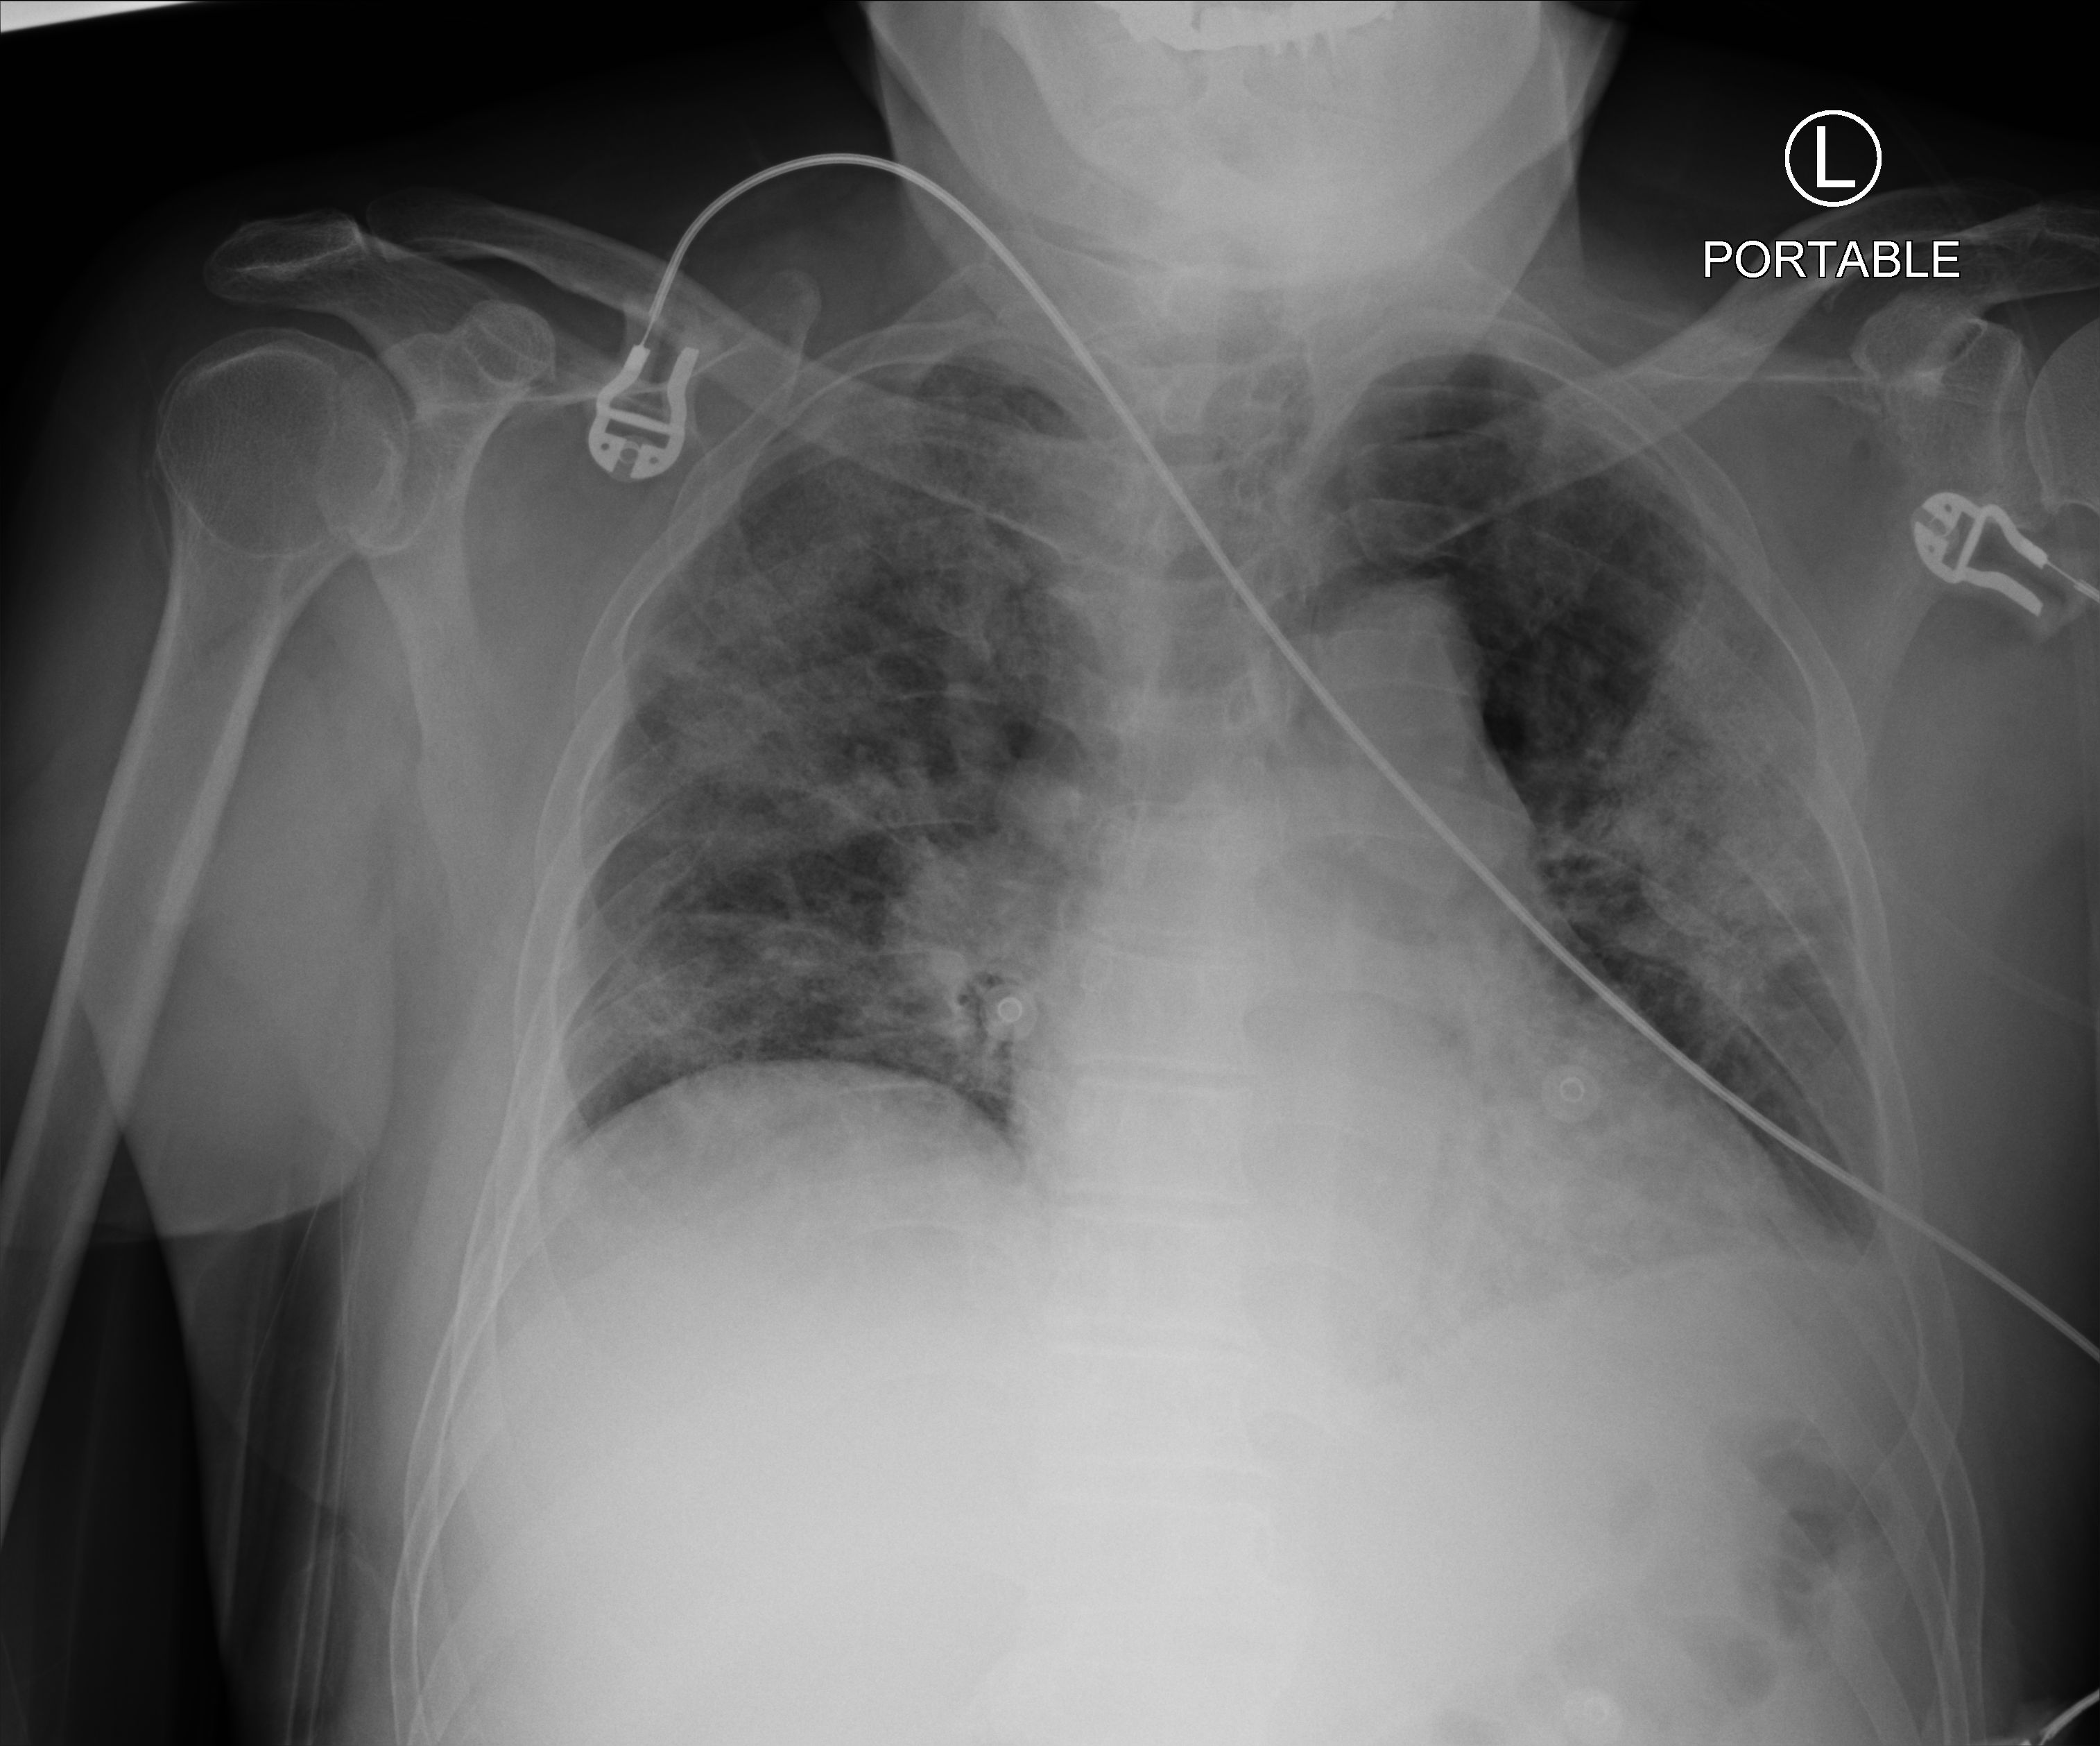
Portable chest radiograph. Patient hospitalised with COVID-19; male, aged 60–74 years.
Hospital-stay facts (about this admission, not read from this image; timing relative to this image not recorded):
- mechanically ventilated during this hospital stay: yes
- admitted to intensive care during this hospital stay: yes
- other chronic lung disease (admission record): no